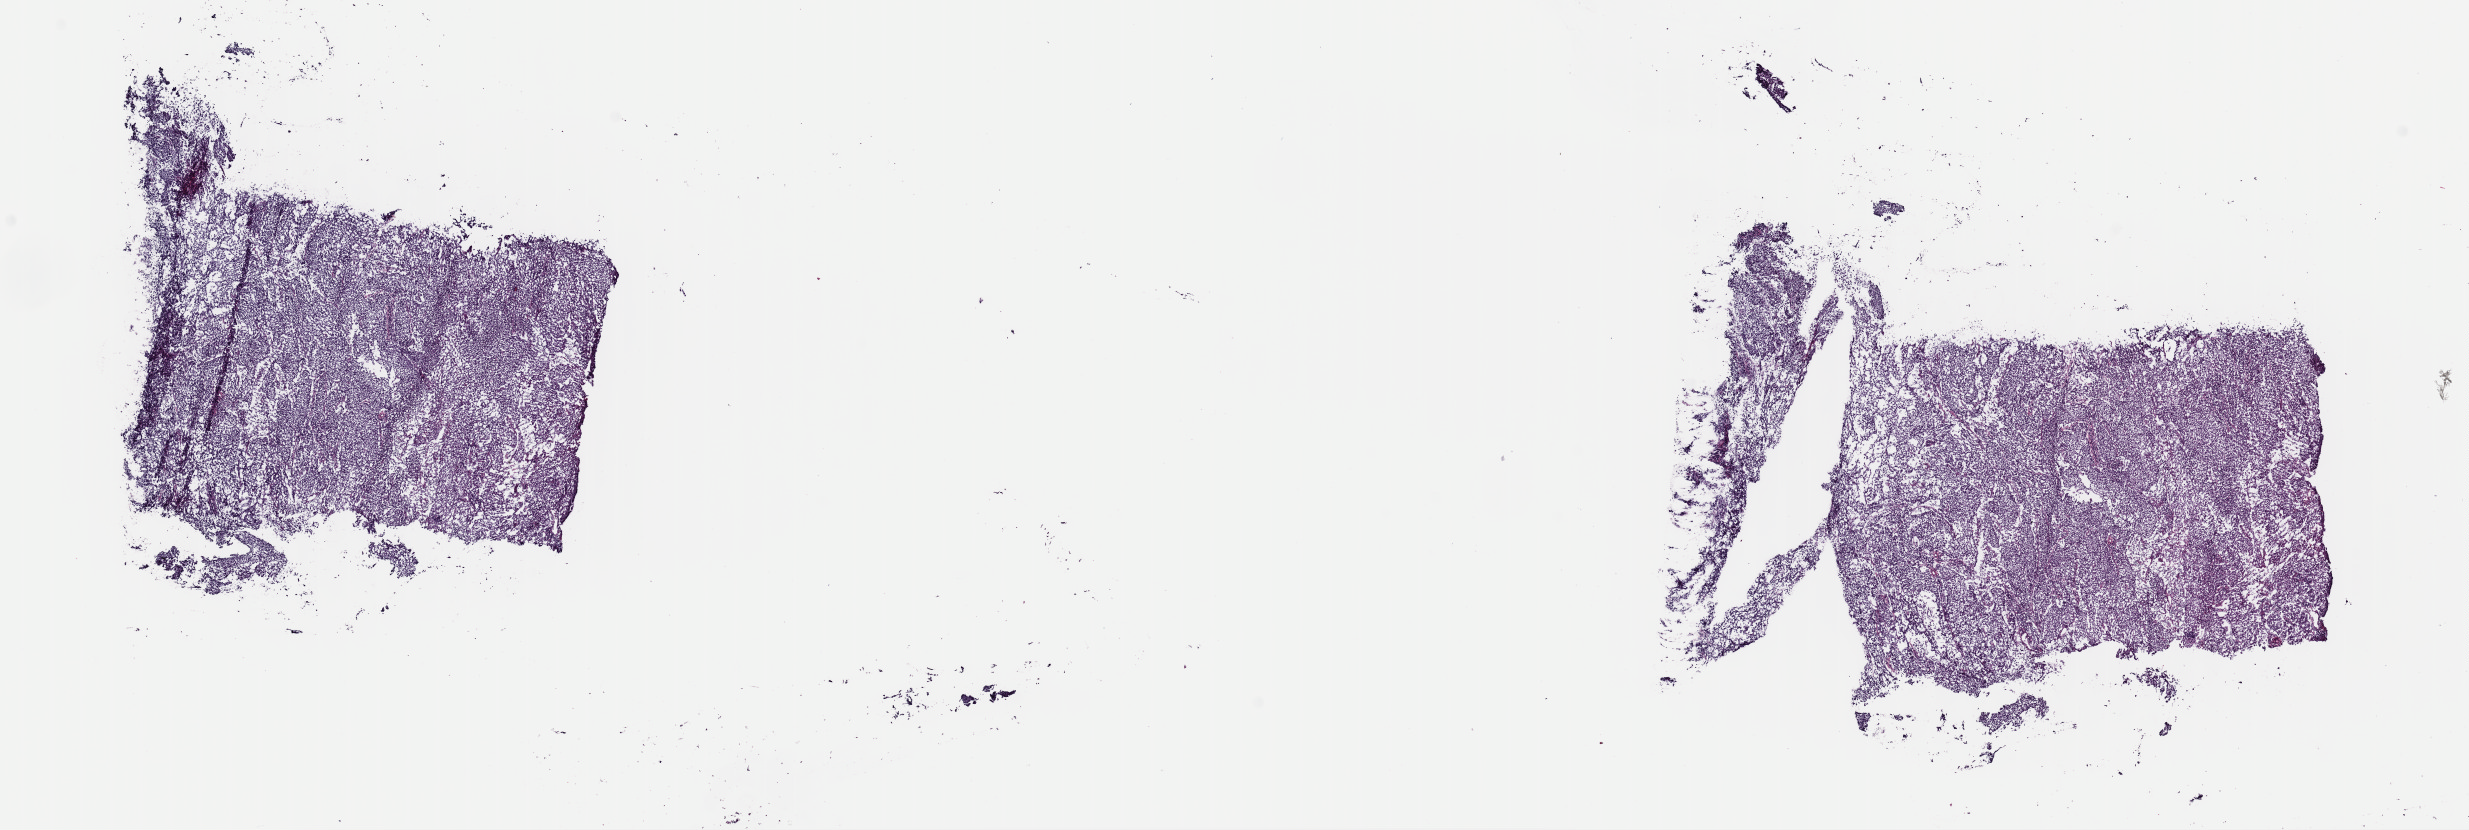
H&E whole-slide image, a low-resolution overview of the entire scanned area, about 19.5 x 6.6 mm (slide scanned at 40x). Frozen section from the top of the tissue portion. Sample: primary tumour, cervix. Female, age 43 years at initial diagnosis. Histologic grade: G2 (moderately differentiated). Composition of this section per pathologist review: tumour cells 100%, tumour nuclei 95%, normal cells 0%, stromal cells 0%, necrosis 0%. Infiltration values recorded for this section: lymphocyte infiltration 1%, monocyte infiltration 0%, neutrophil infiltration 0%.
Lymph nodes positive (case pathology): 0 of 14 examined. Pathologic diagnosis: Squamous cell carcinoma, NOS. FIGO stage: II.